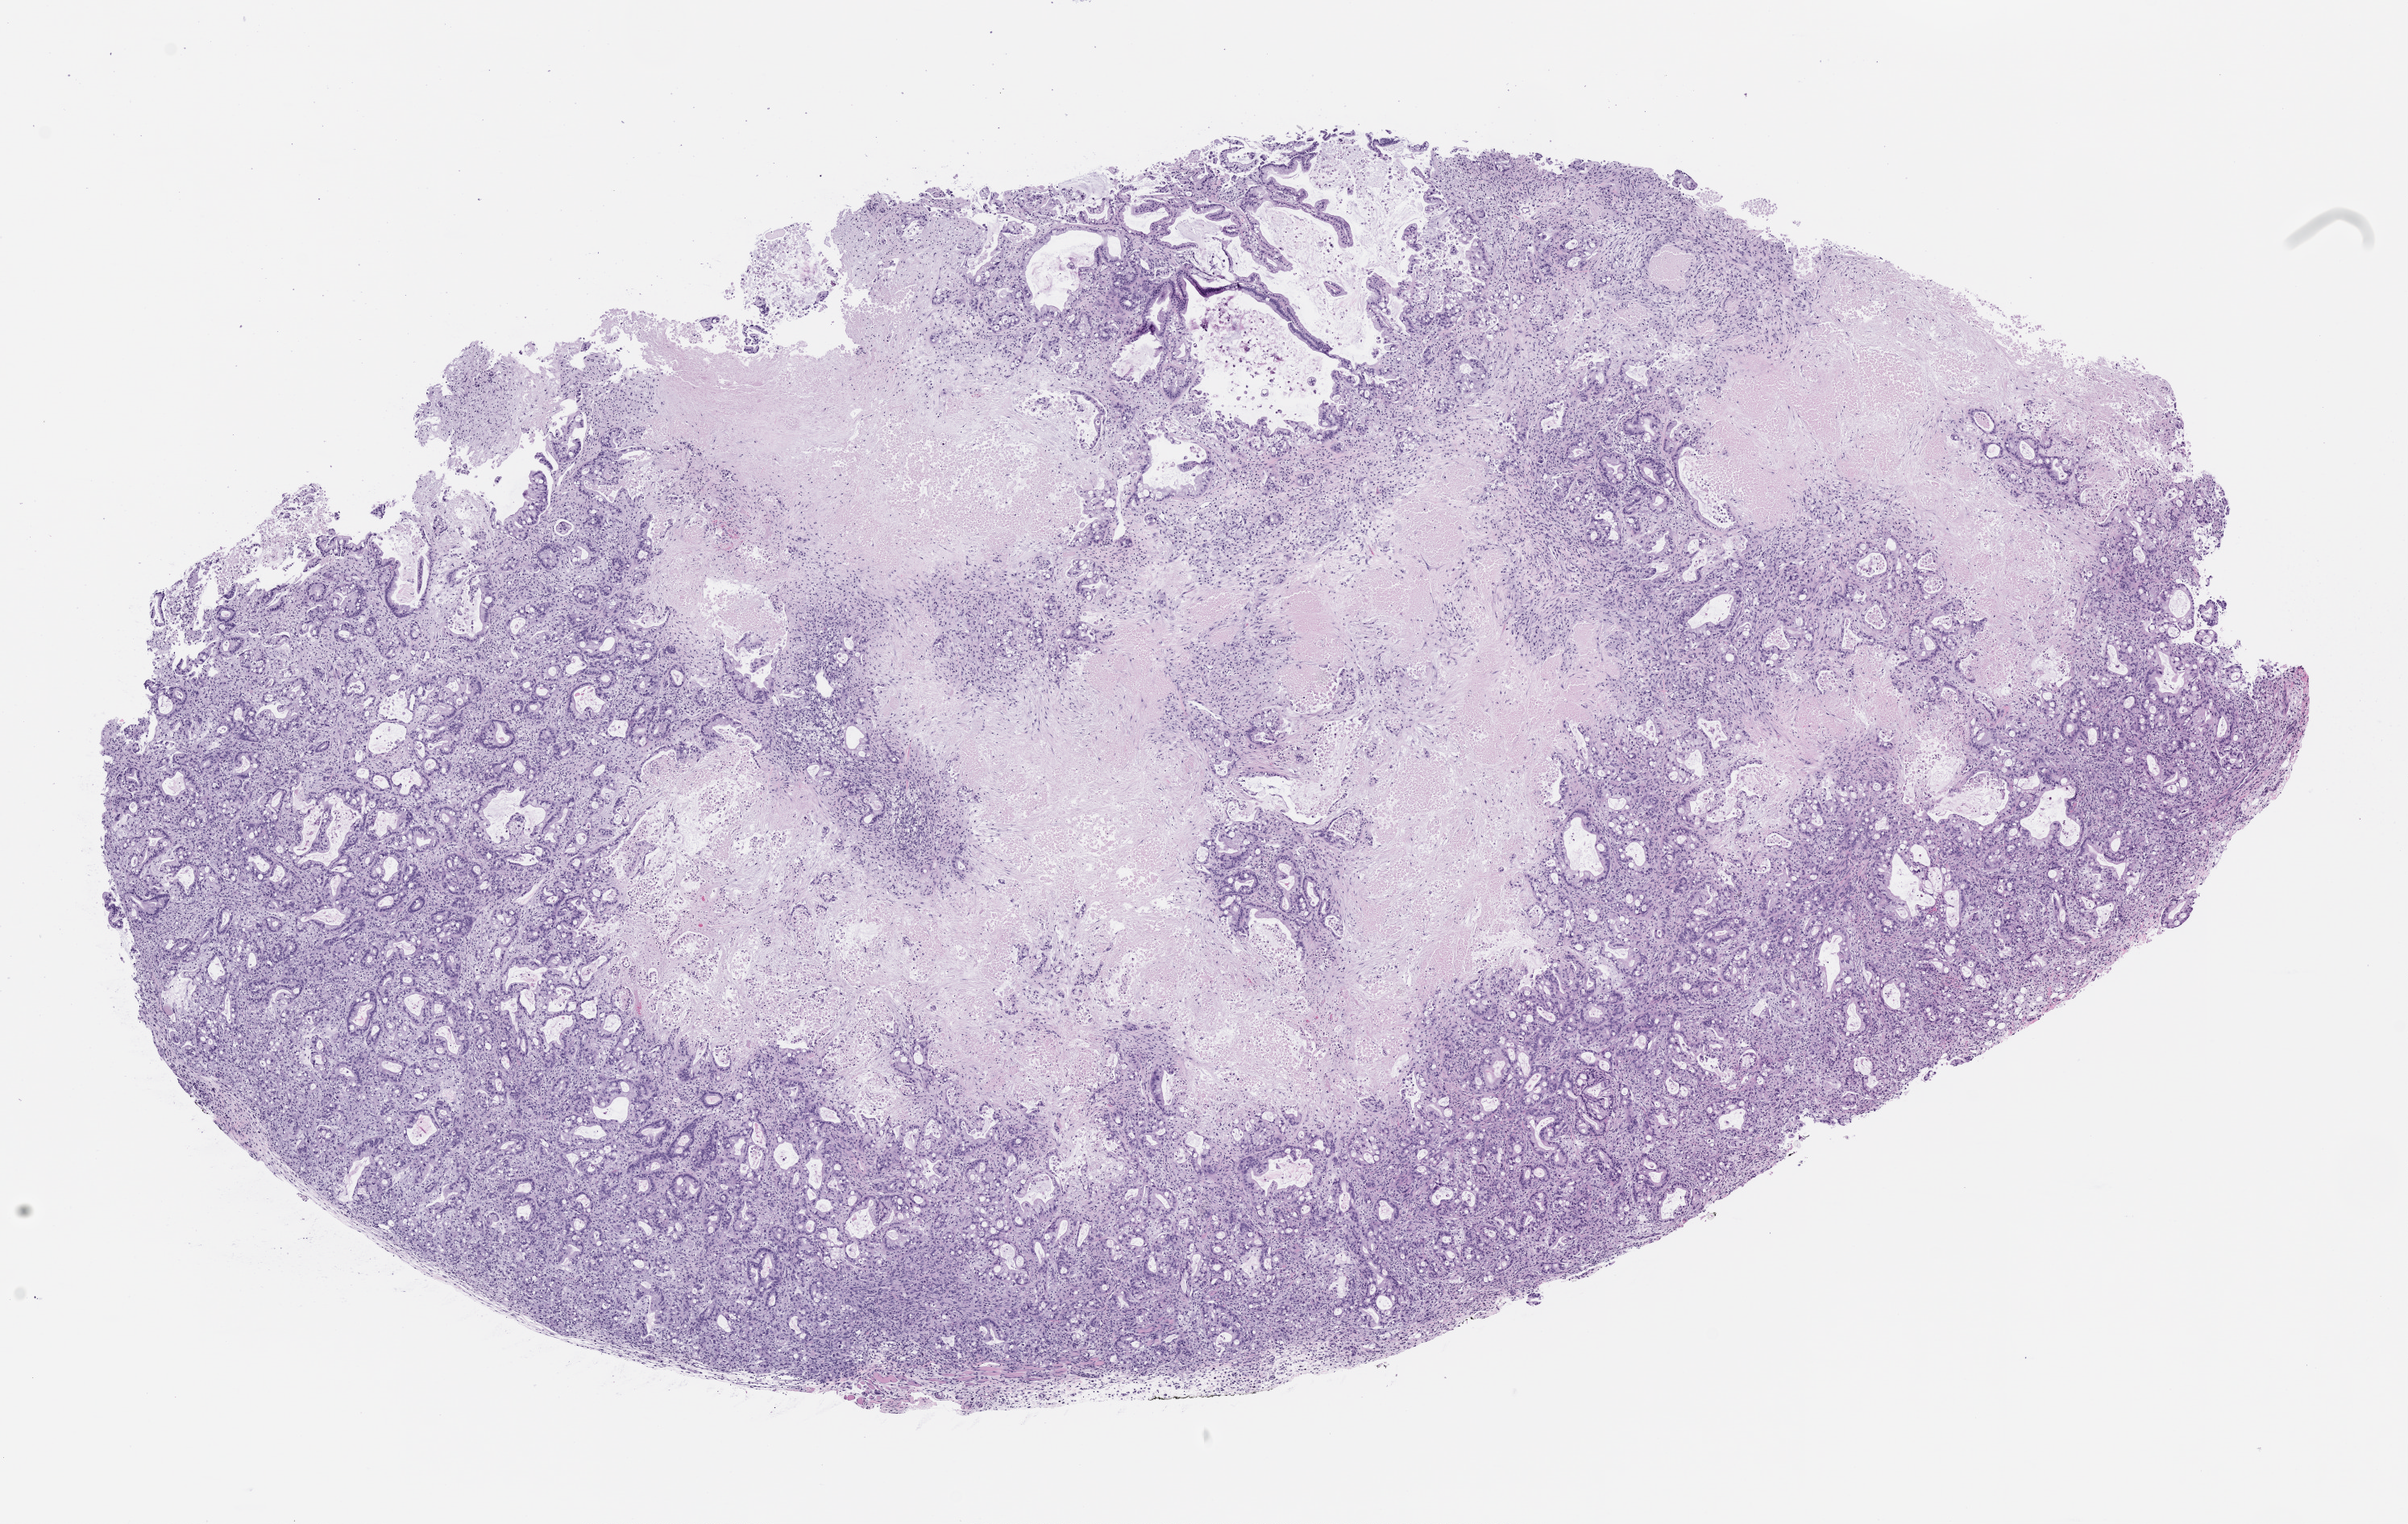
Haematoxylin and eosin whole-slide image of a patient-derived xenograft (PDX) tumor grown in a mouse, passage 2, whole scanned area (about 12.0 x 7.6 mm) shown as a low-resolution overview, formalin-fixed, paraffin-embedded (FFPE) tissue, originating tumor site category: pancreas.
Originating patient diagnosis: Pancreatic Adenocarcinoma.